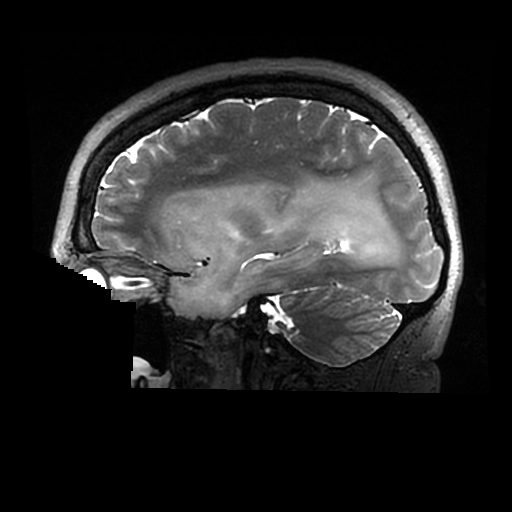
Brain MRI from a brain-tumour surgery series, one sagittal slice. Position 198 of 320 along the scan axis. 512 × 512 image matrix, field of view 240 × 240 mm. From the clinical record (not read from this slice): histopathology: Astrocytoma; WHO grade: 2; IDH mutation: yes.
Structures marked on this image (expert manual segmentation):
- tumour: bounding box [x1, y1, x2, y2] px = [170, 181, 401, 319]